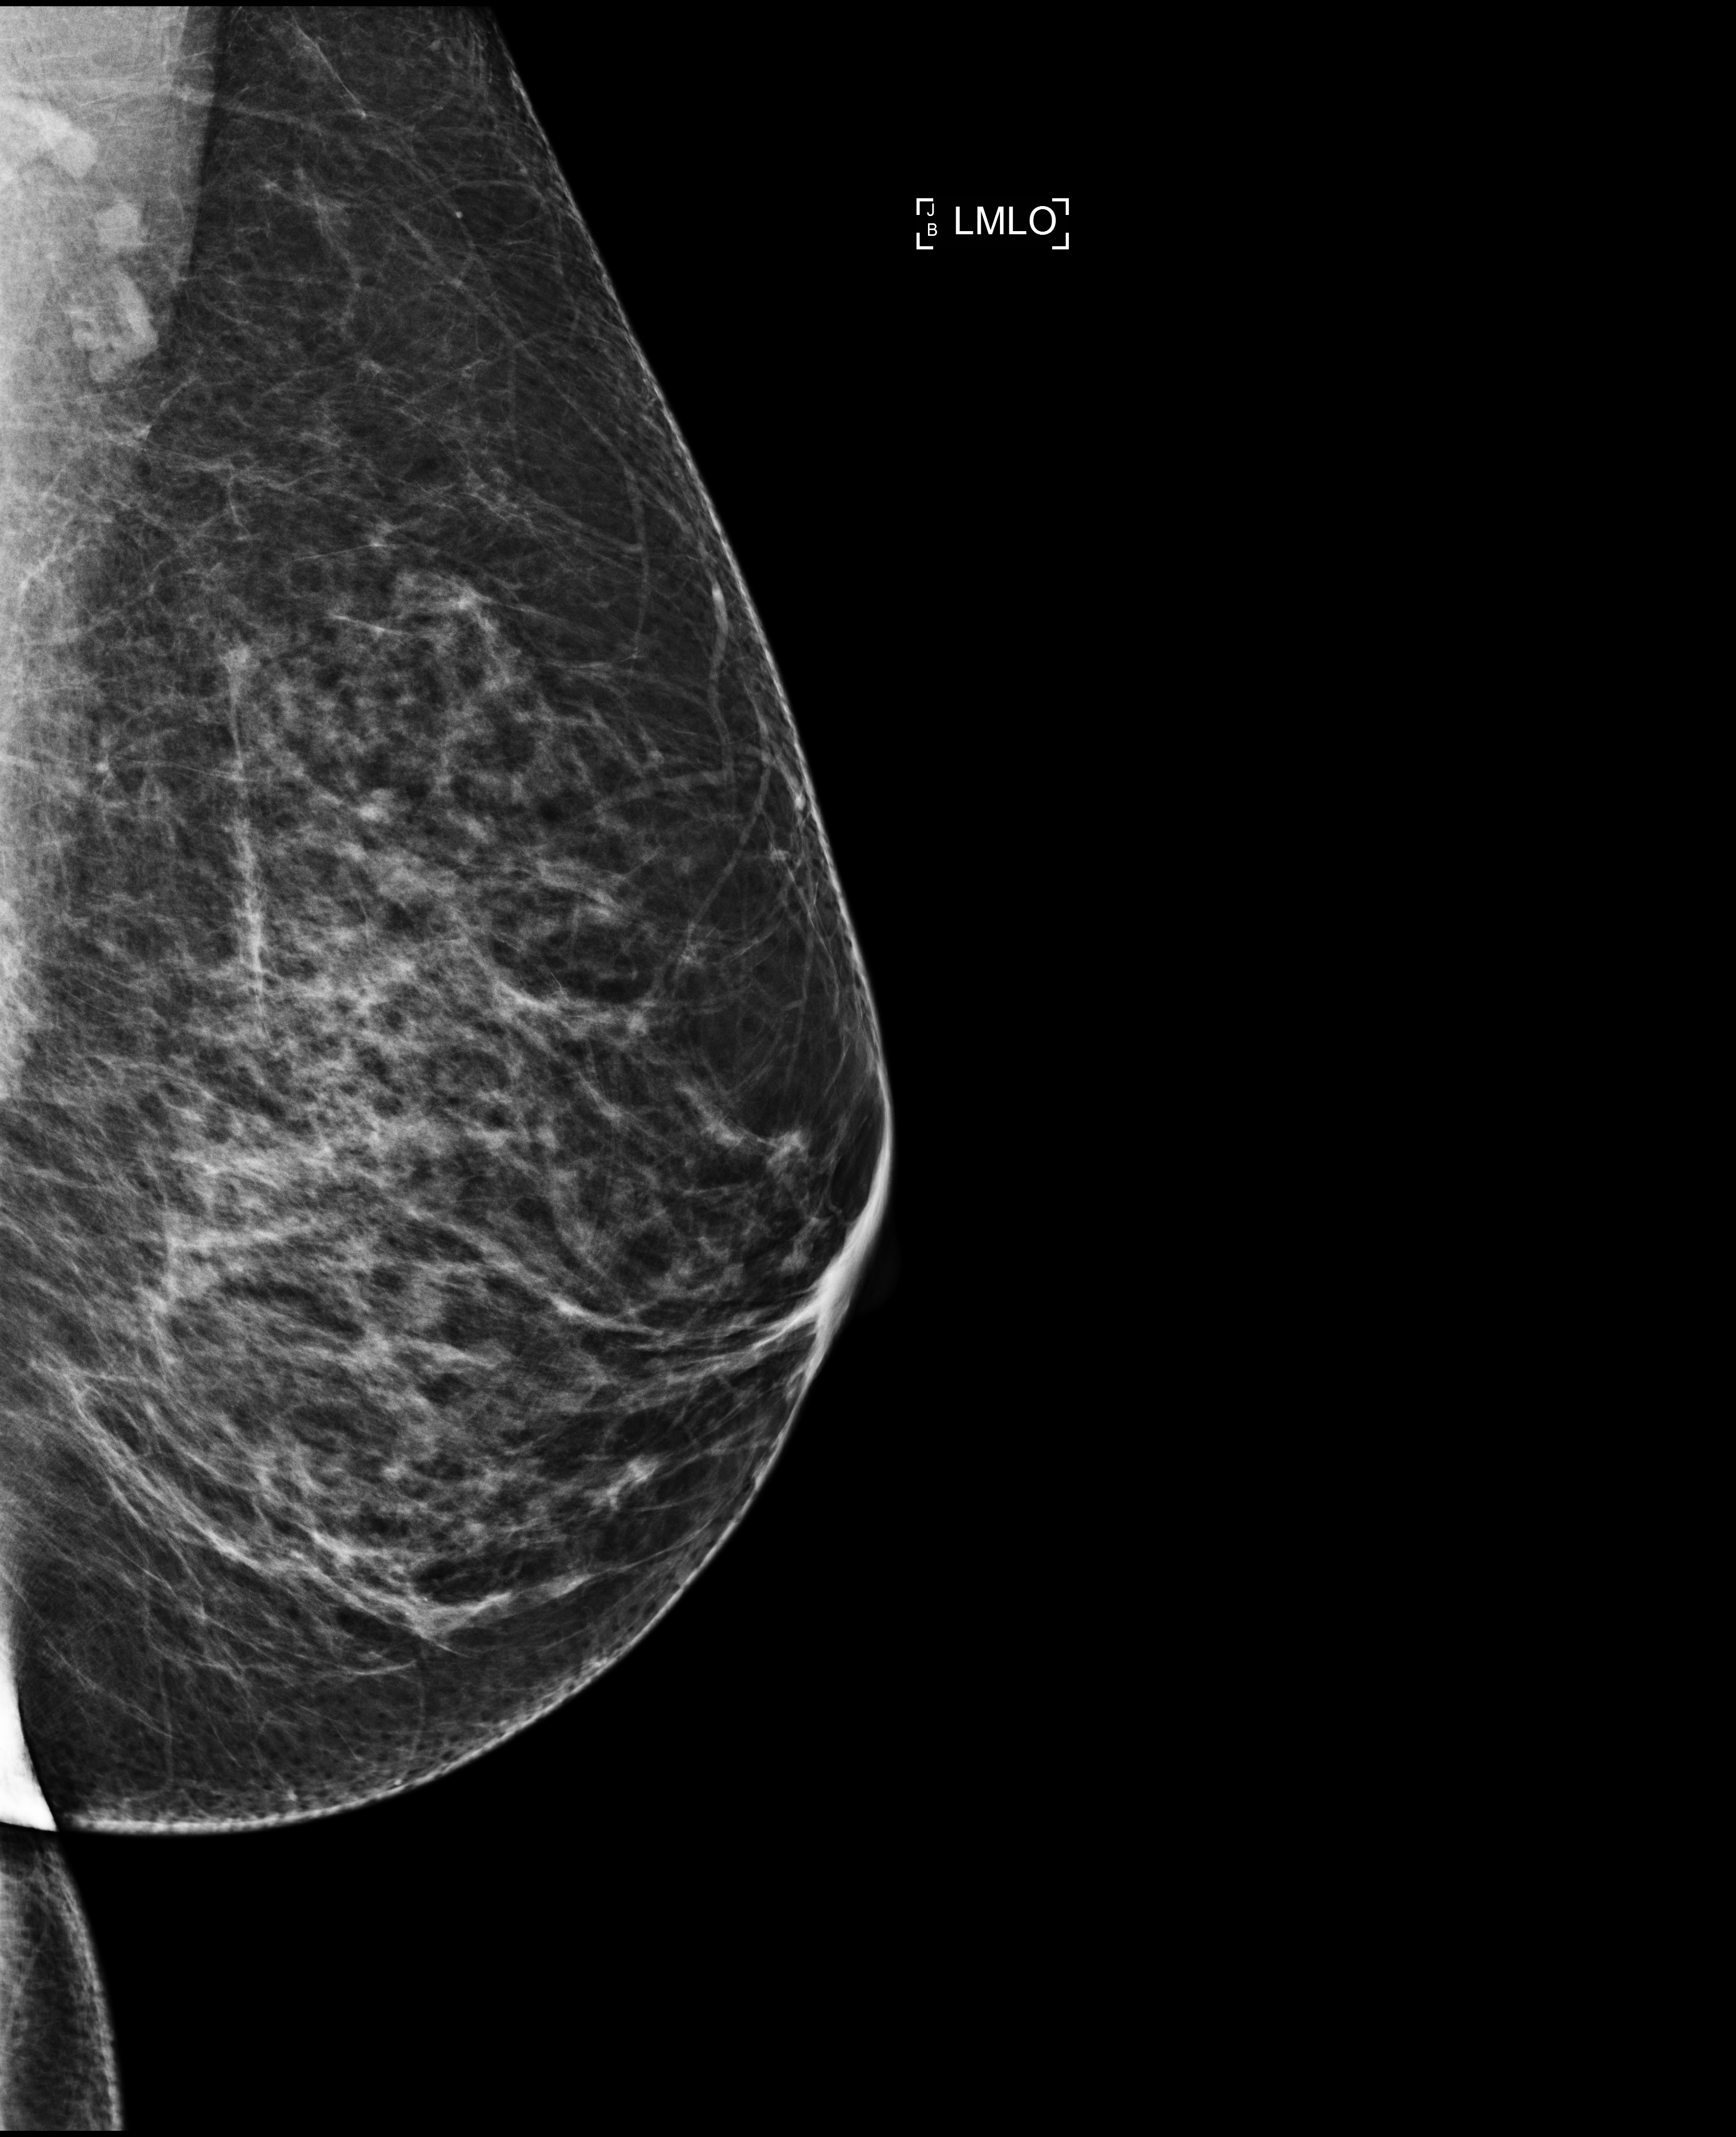
Screening examination, compressed breast thickness 71 mm, system: Selenia Dimensions.
Image type: full-field digital mammogram. Breast: left. Projection: MLO view.